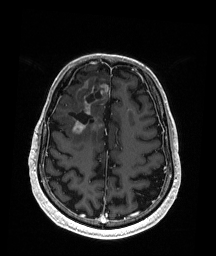
Brain MRI from a brain-tumour surgery series, one axial slice. Slice 60 of 192 in the series (ordered by position). T1-weighted post-contrast. 216 × 256 image matrix. From the clinical record (not read from this slice): histopathology: Astrocytoma; WHO grade: 3; IDH mutation: yes.
Annotated regions visible in this slice (expert manual segmentation):
- previous resection cavity: box from (x=70, y=87) to (x=101, y=124) px
- tumour: (x=71, y=82)–(x=109, y=137)